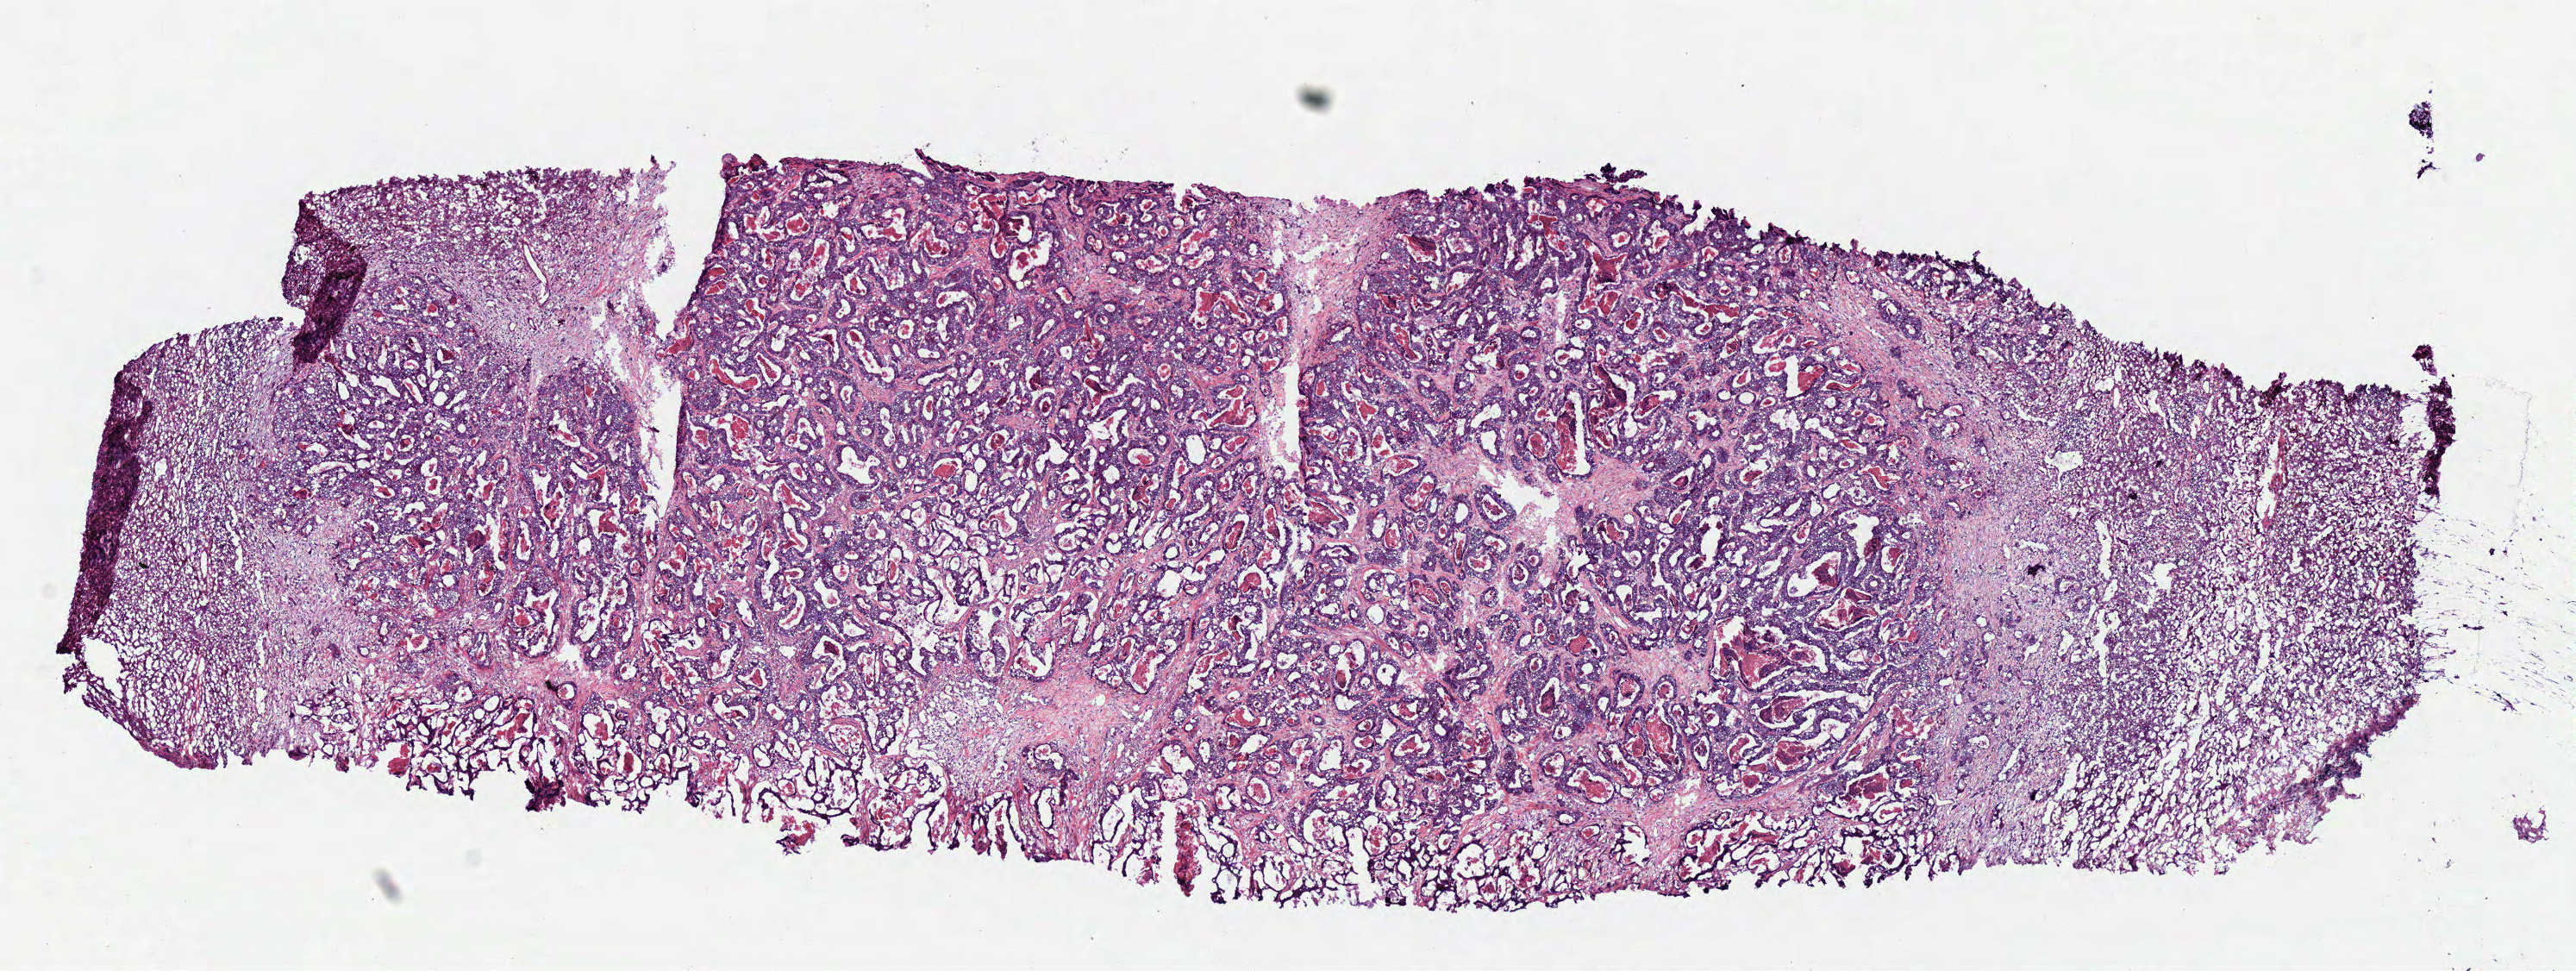
H&E whole-slide image, low-resolution overview of the scanned area, about 11.7 x 4.4 mm; frozen section; colon, recurrent tumour sample. Female, age 51 years at initial diagnosis. Pathologist review of this section (percent, as recorded): tumour cells 72%, tumour nuclei 85%, normal cells 0%, stromal cells 10%, necrosis 18%.
This section: recurrent tumour. Patient diagnosis: Adenocarcinoma, NOS (sigmoid colon).